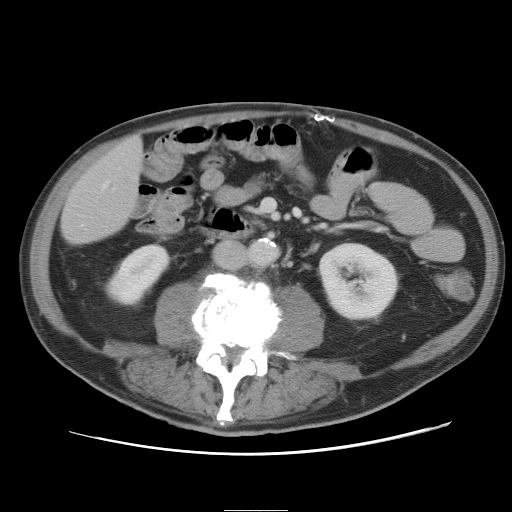
Contrast-enhanced abdominal CT, one axial slice; position 8 of 89 along the scan axis; intravenous contrast given; soft-tissue window (W 400 / L 40 HU); 512 × 512 image matrix, field of view 375 × 375 mm. Male patient, age 69 years. From the clinical record (not read from this slice): diagnosis: colorectal cancer liver metastases, imaged before liver resection; multiple liver metastases: no; largest metastasis: 8.5 cm; disease in both lobes: no.
Annotated regions visible in this slice (manually delineated by an expert):
- hepatic veins: bounding box <104,184,107,187> (left, top, right, bottom; pixels)
- liver: <62,137,144,244>
- planned liver remnant (the part of the liver to remain after resection): <62,137,144,244>